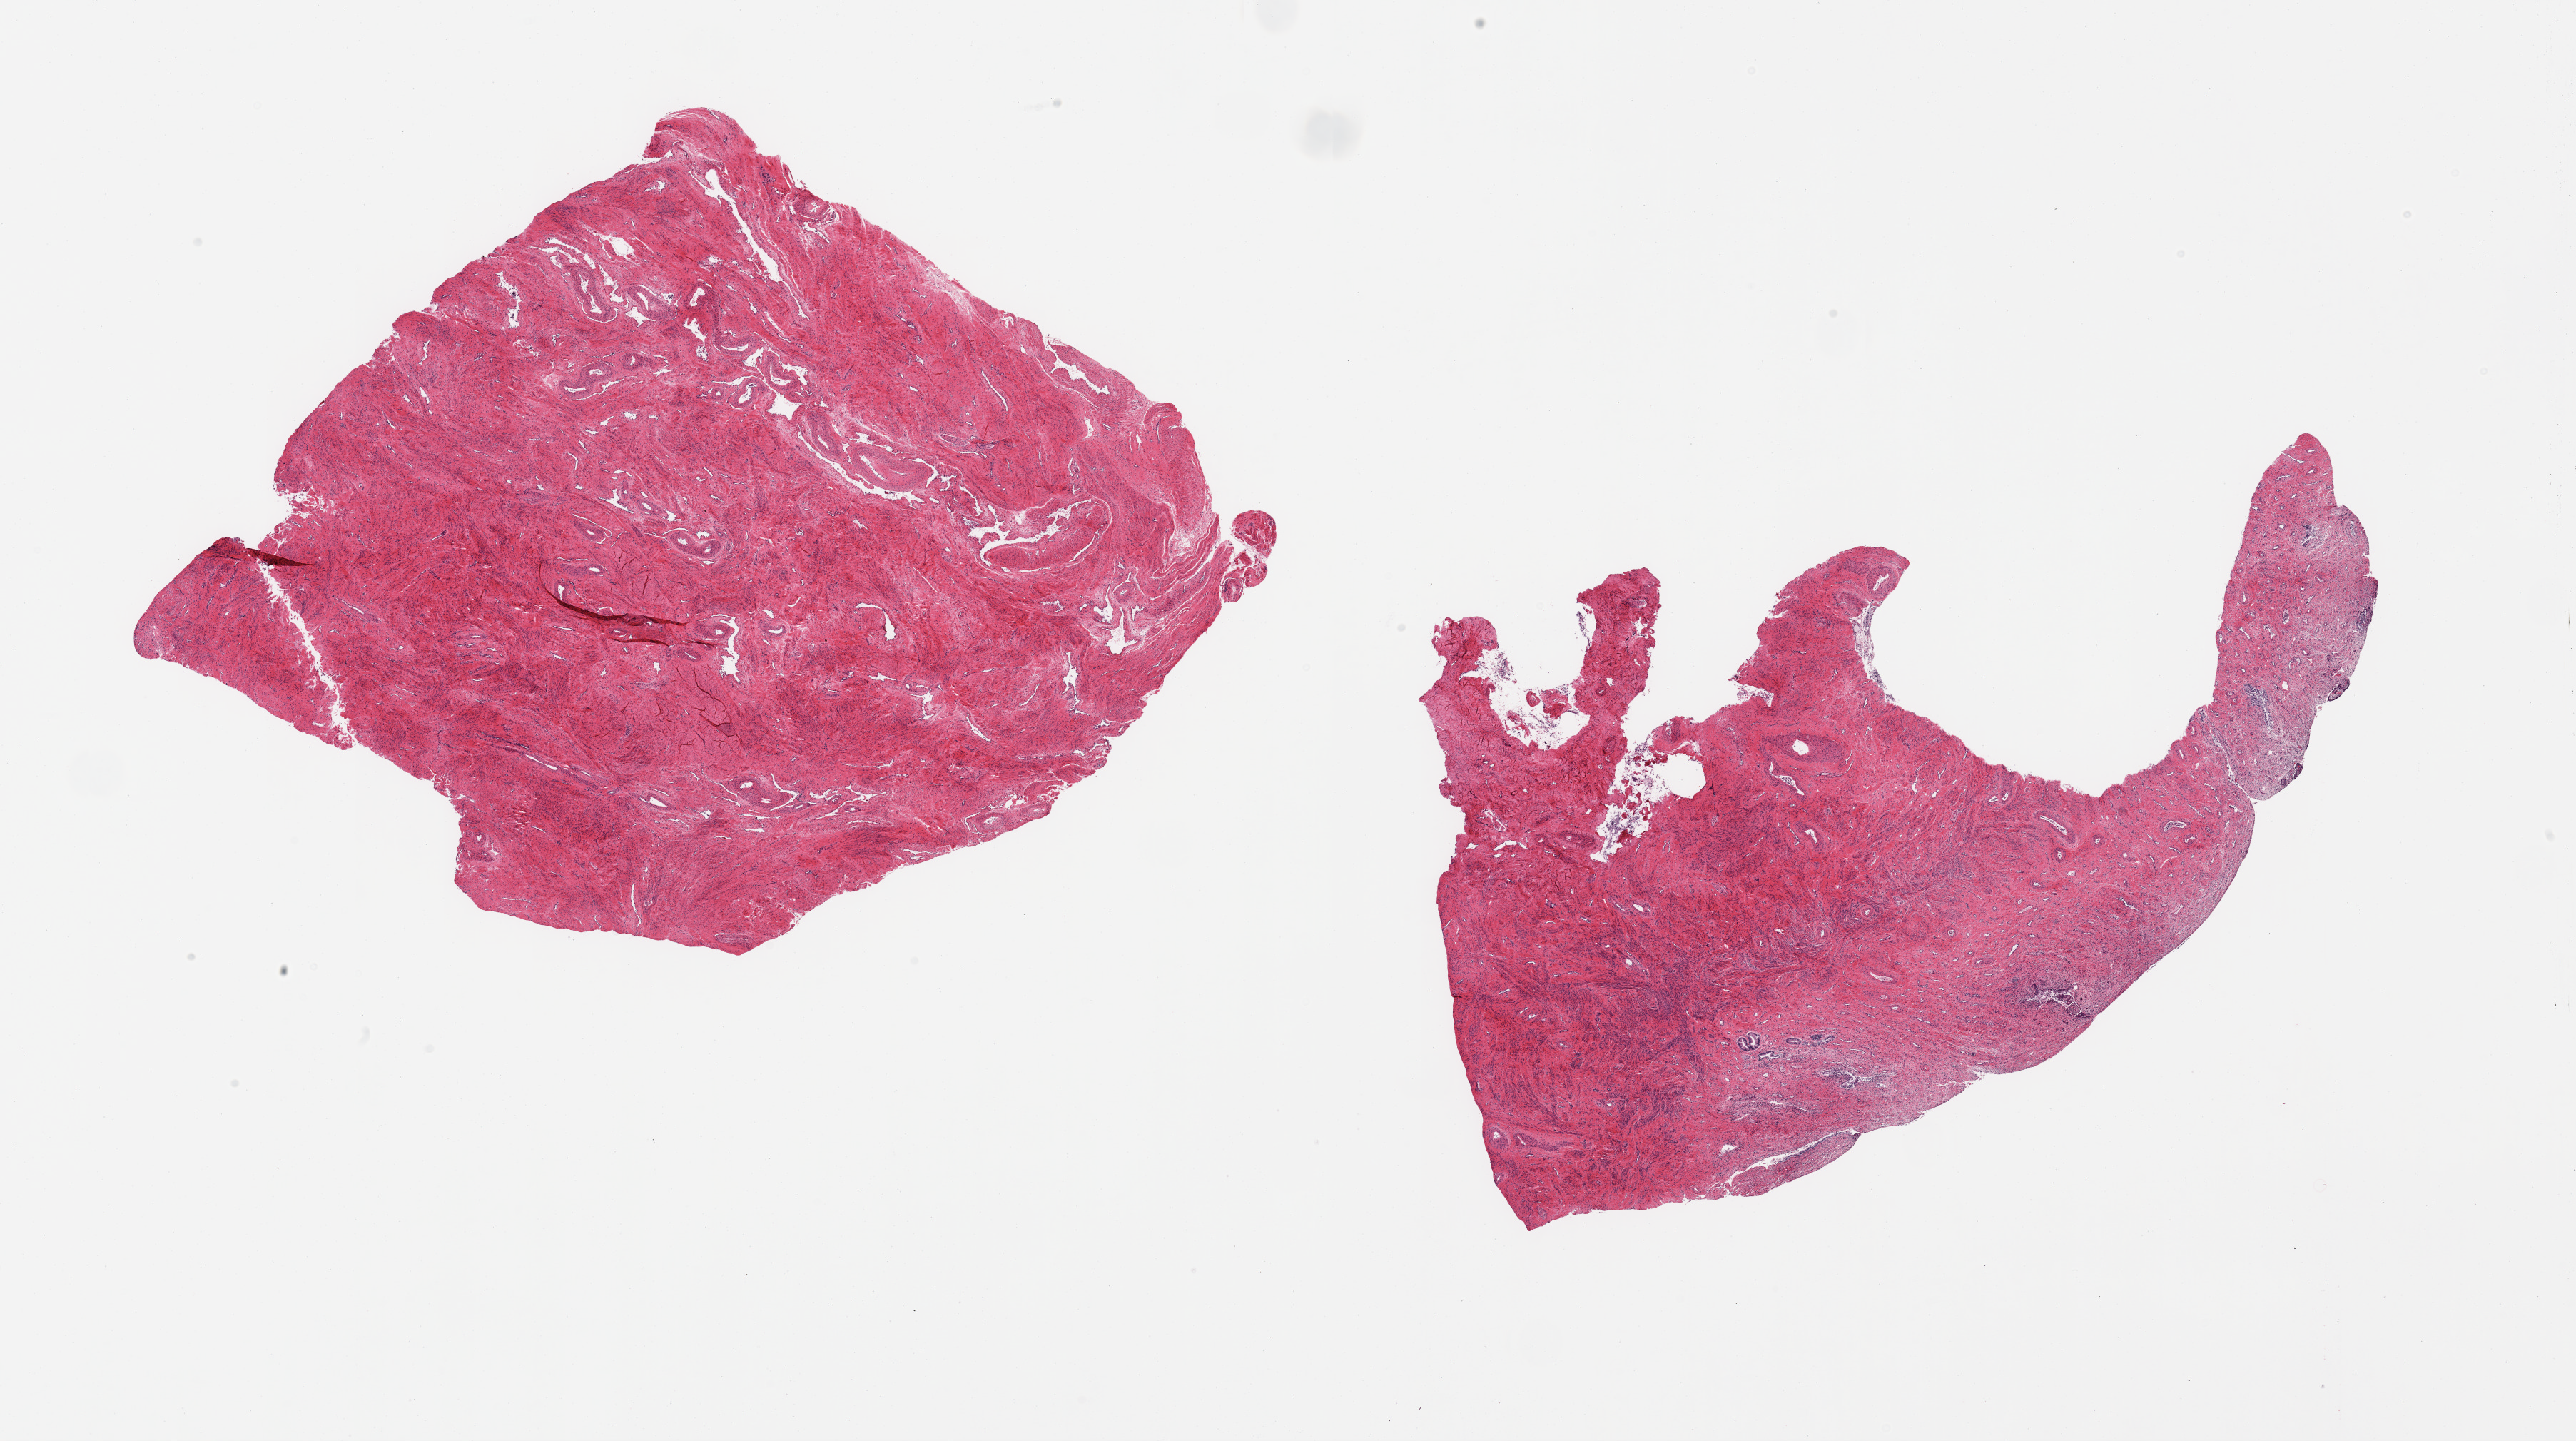
Digitized haematoxylin and eosin-stained section, brightfield, low-resolution overview of the scanned area, about 28.5 x 16.0 mm (from a 20x scan); PAXgene-fixed, paraffin-embedded tissue; section of uterus (target tissue); donor tissue sample.
Reviewer comment on this tissue sample: 2 pieces; myometrium with scant glandular component in one piece, ? lower uterine segment.